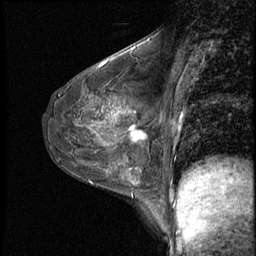
Breast MRI (dynamic contrast-enhanced), one sagittal slice. Slice 30 of 50 in the series (ordered by position). 3 images stored at this slice position (order not interpretable as contrast timing). 1.5 T. TE 4.2 ms, TR 8.7 ms. 256 × 256 image matrix, field of view 180 × 180 mm. Patient: female, 43 years. From the clinical record (not read from this slice): setting: breast cancer imaged before/during neoadjuvant chemotherapy; receptor status: HR-positive, HER2-negative.
Outlined on this slice (semi-automatic segmentation, software-assisted and operator-edited):
- analysis volume of interest (the breast-tissue region the enhancement analysis was run in; not a lesion): bounding box <122,109,159,155> (left, top, right, bottom; pixels)
- tumour enhancement mask (voxels above the 140 % enhancement threshold inside the analysis volume of interest): <122,110,147,142>